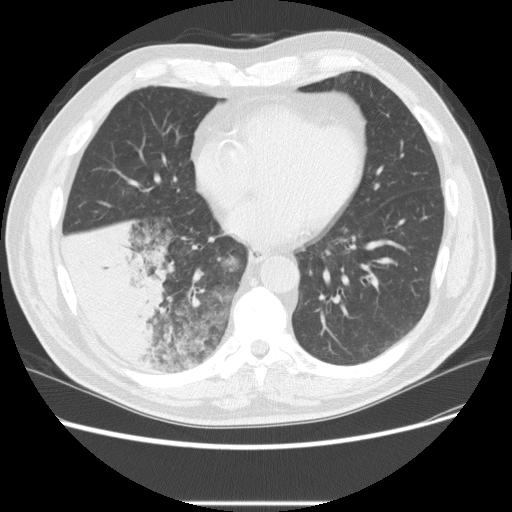
Low-dose screening chest CT, one axial slice; slice 89 of 233 in the series (ordered by position); lung window (W 1500 / L -600 HU); 2.5 mm slice thickness; 512 × 512 image matrix, field of view 380 × 380 mm.
Annotated regions visible in this slice (expert manual segmentation):
- lesion 3 (tumor, lower lobe of right lung): box from (x=64, y=217) to (x=176, y=353) px